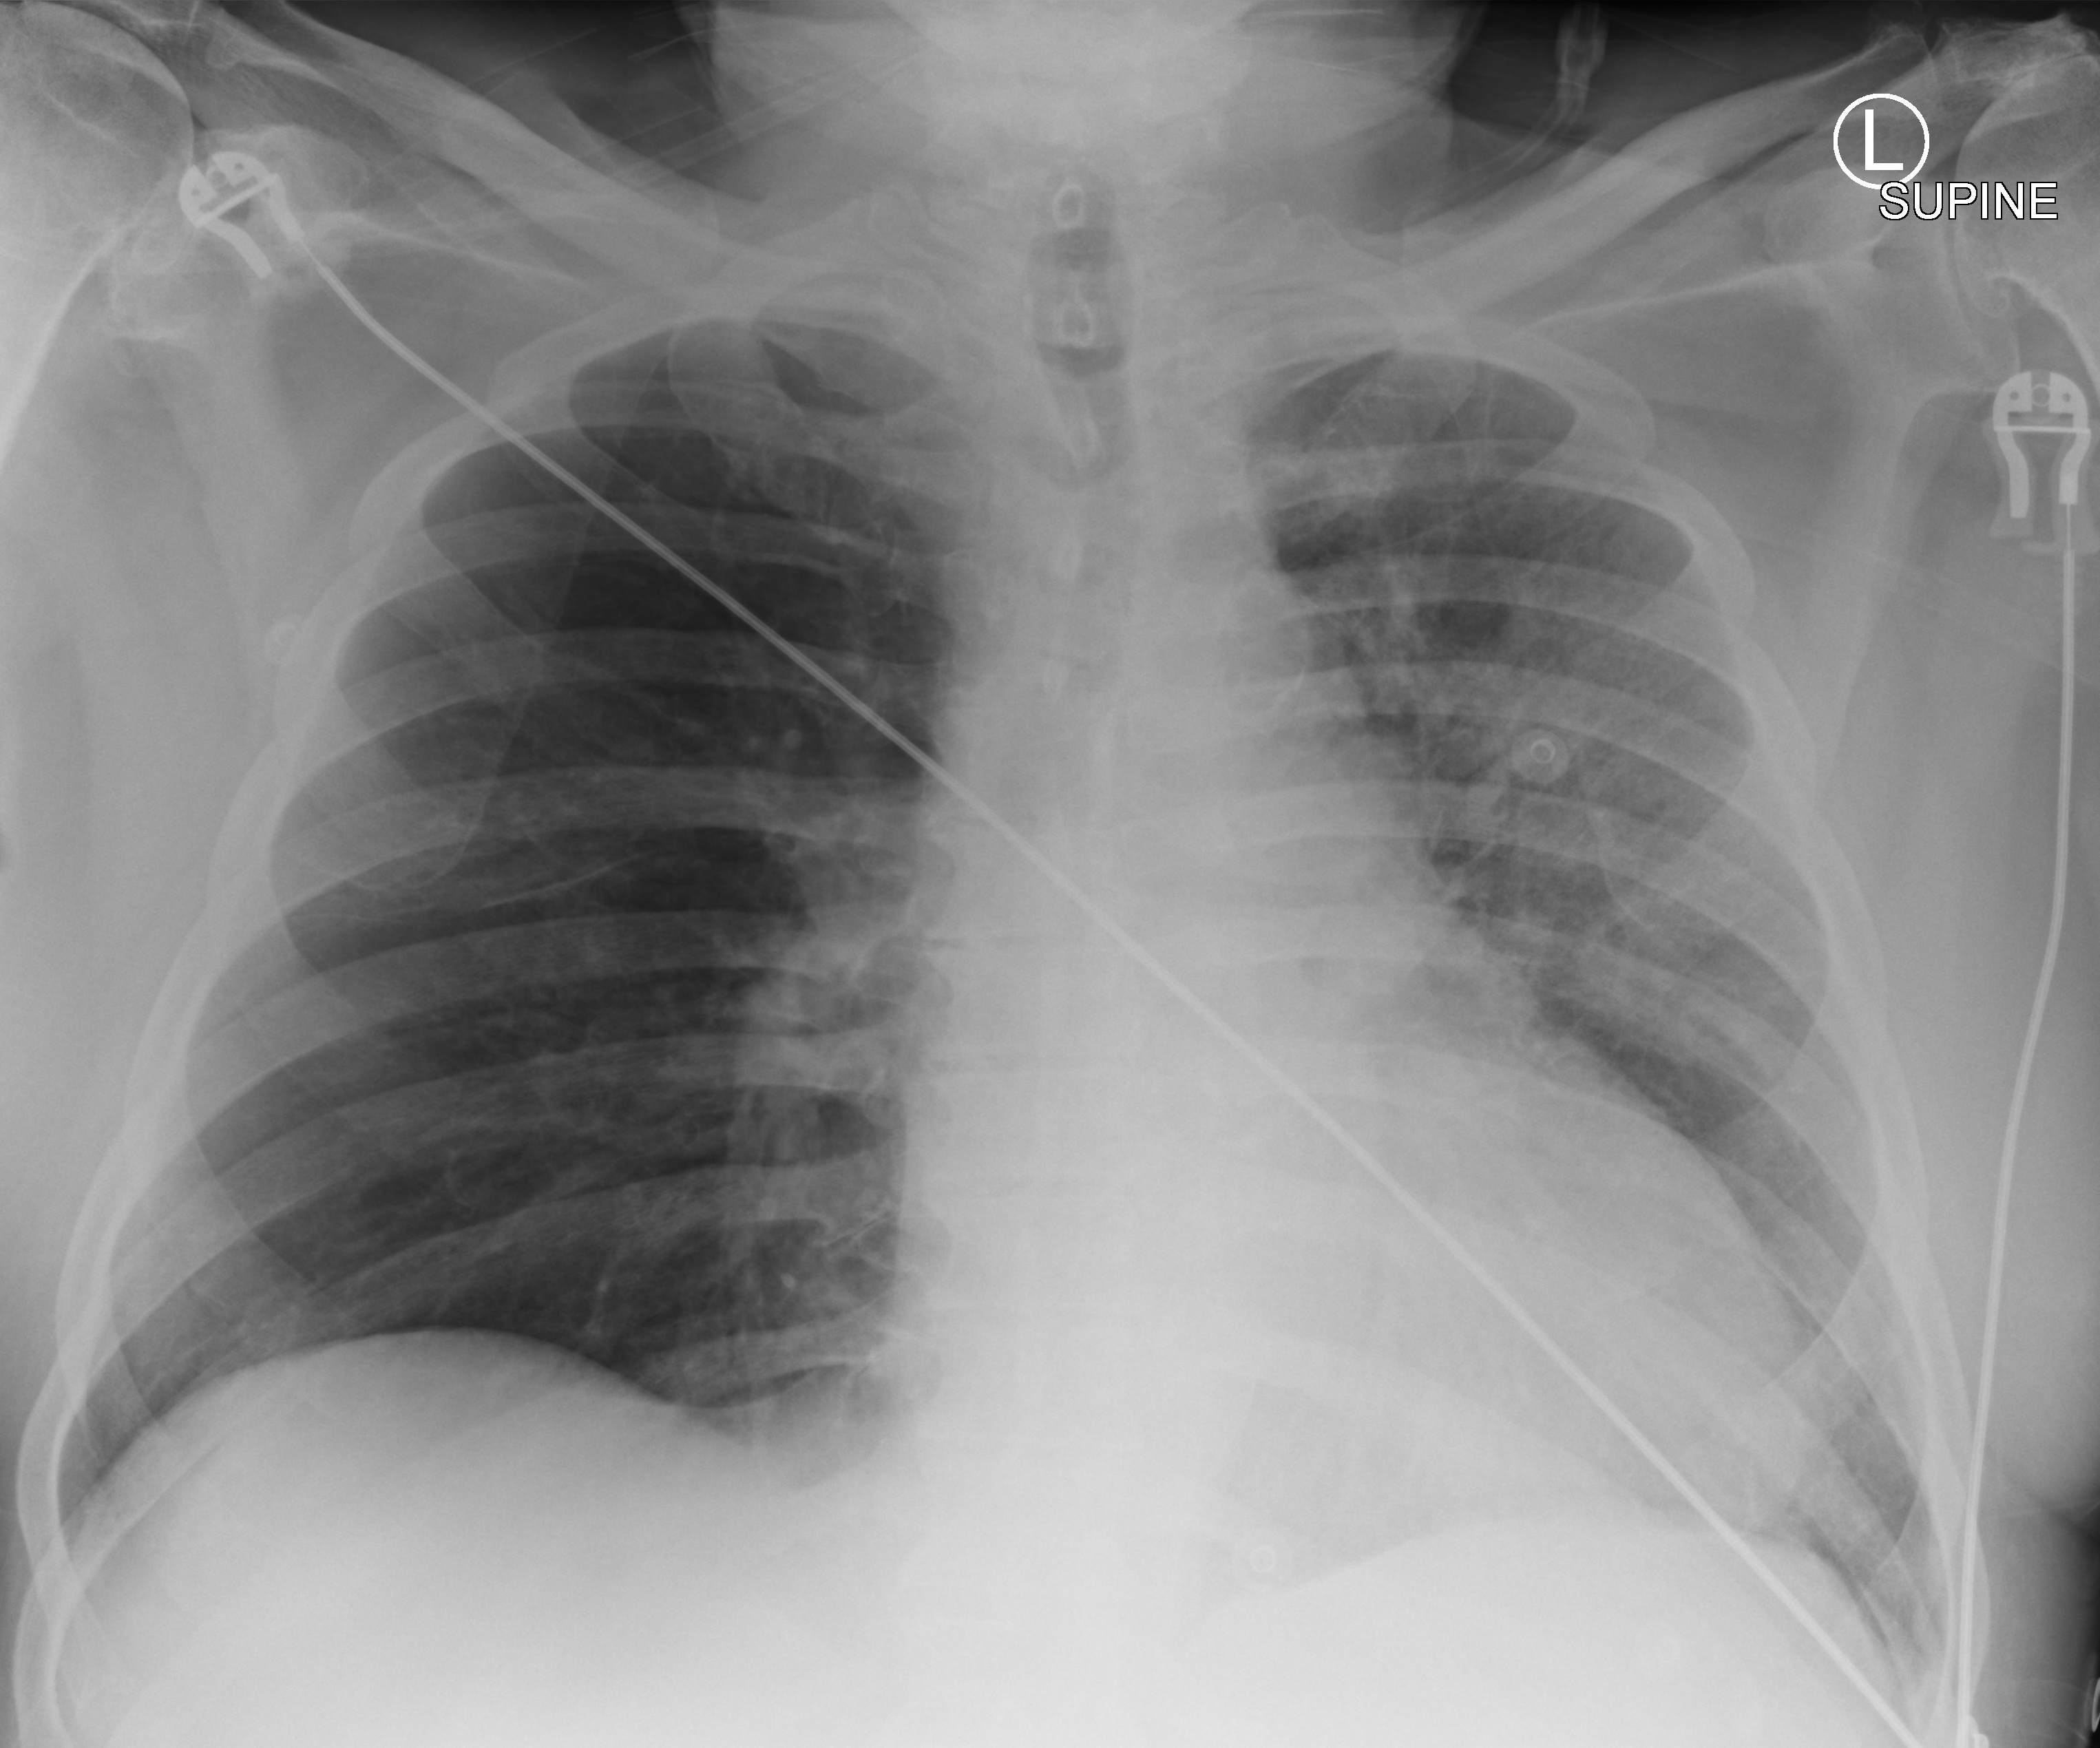
Chest X-ray (portable), anteroposterior (AP) projection. Male patient hospitalised with COVID-19, age 60–74 years.
Hospital-stay facts (about this admission, not read from this image; timing relative to this image not recorded): admitted to intensive care during this hospital stay: yes; diabetes (admission record): yes.